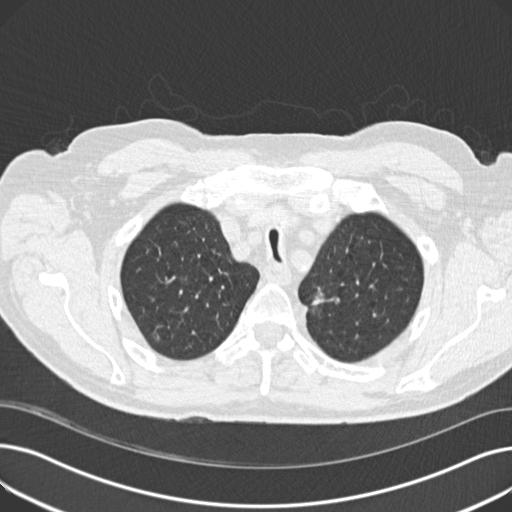
Low-dose screening chest CT, one axial slice. Slice 151 of 191 in the series (ordered by position). Reconstruction kernel B30f. 120 kVp. Lung window (W 1500 / L -600 HU). 2 mm slice thickness. 512 × 512 image matrix, field of view 370 × 370 mm.
Annotated regions visible in this slice (outlined manually by an expert reader):
- lesion 1 (tumor, upper lobe of left lung): box from (x=313, y=288) to (x=324, y=305) px